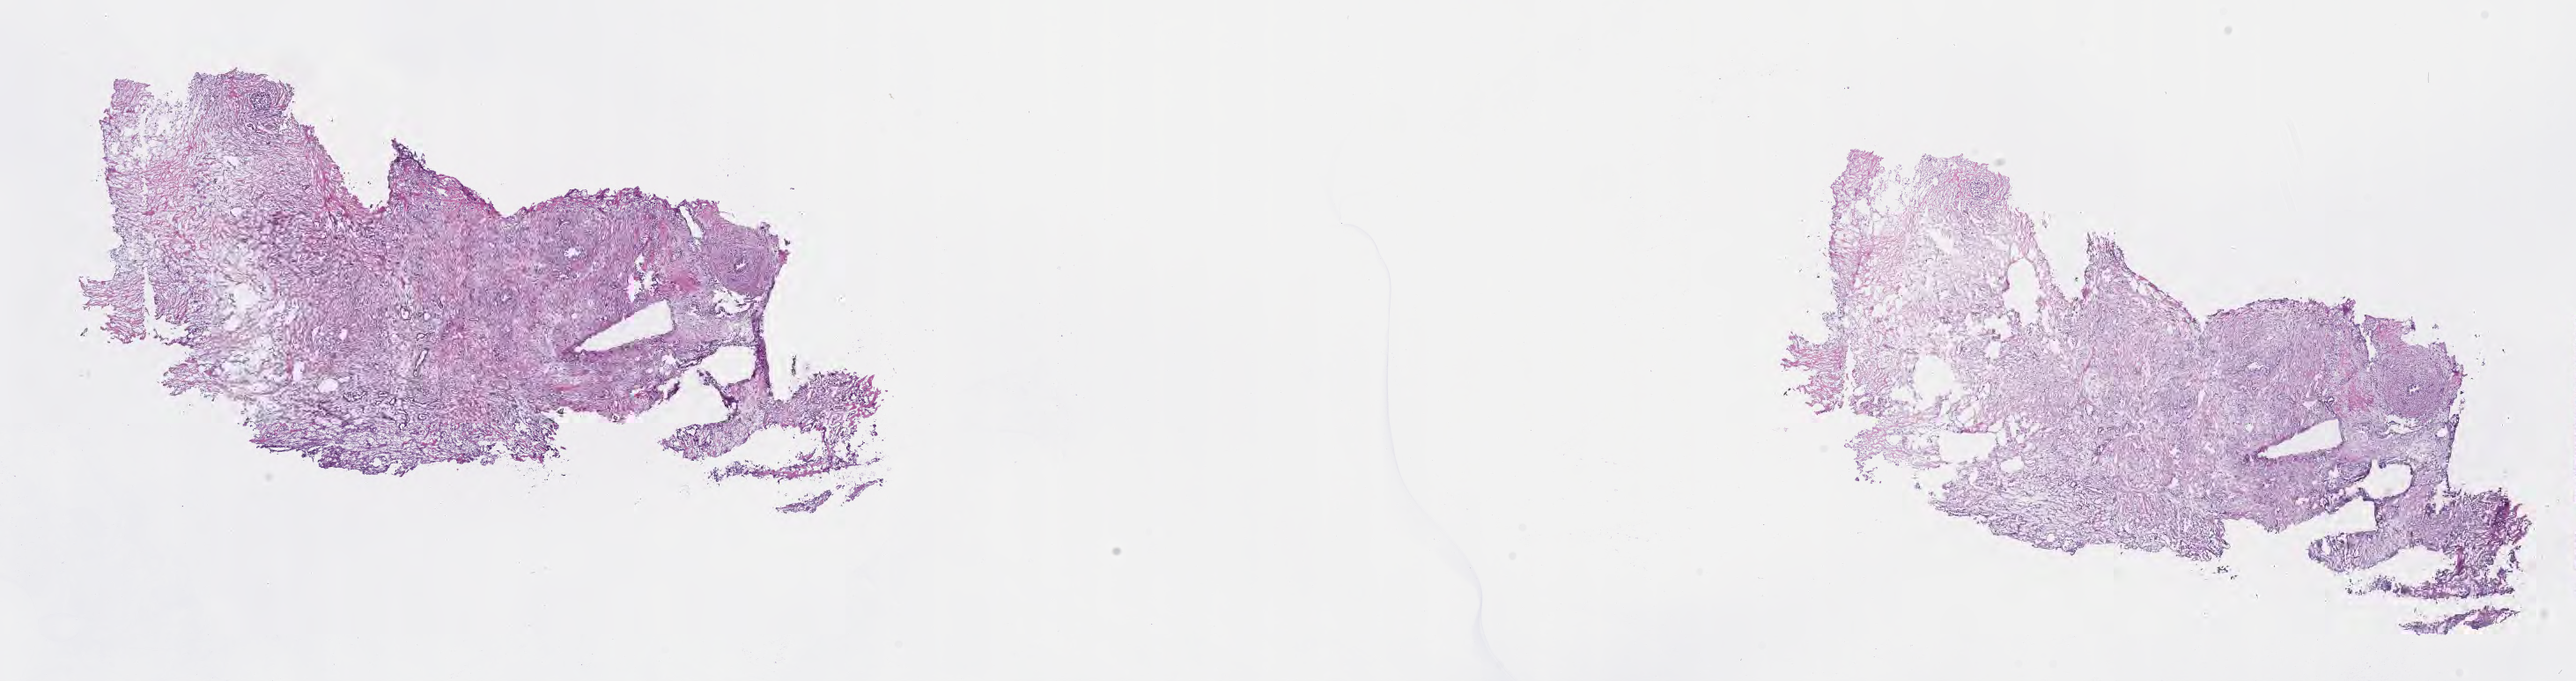
Whole-slide image, H&E stain, a low-resolution overview of the entire scanned area, about 23.6 x 6.2 mm. Frozen section. Primary tumor. Anatomic site: tail of pancreas. Female patient; age at initial diagnosis 68 years. Composition of this section per pathologist review: tumor cells 90%, tumor nuclei 50%.
Diagnosis: Infiltrating duct carcinoma, NOS.